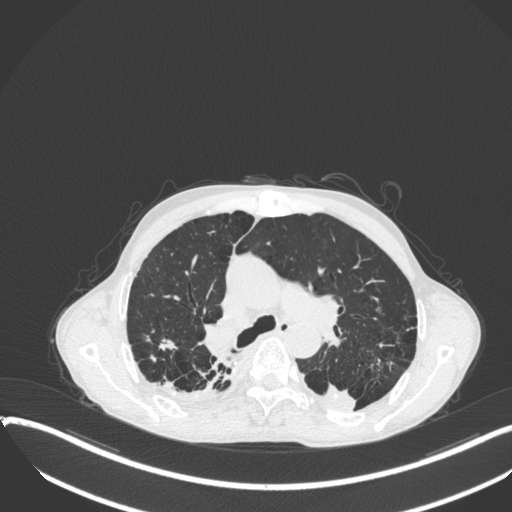
Chest CT, one axial slice. Reconstruction kernel B31f. 120 kVp. Lung window (W 1500 / L -600 HU). 512 × 512 image matrix, field of view 400 × 400 mm. Male patient, age 57 years. From the clinical record (not read from this slice): clinical TNM (as recorded): T4 N0 M0.
Outlined on this slice (bounding box drawn by a radiologist):
- lung tumour (recorded histology: squamous cell carcinoma): bounding box [x1, y1, x2, y2] px = [307, 373, 362, 416]